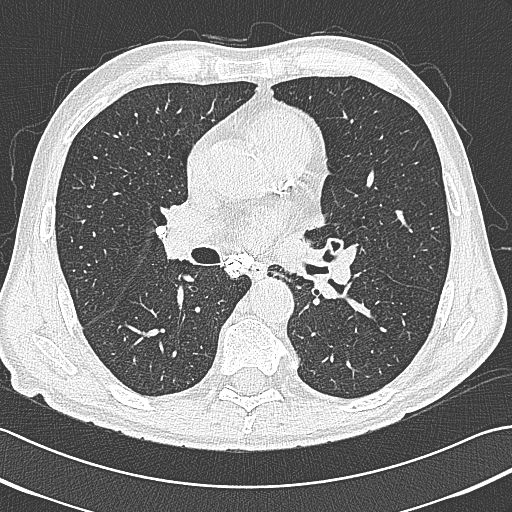
Axial slice from a low-dose chest CT screening exam; baseline screening round; lung window (W 1500 / L -600 HU); 1 mm slice thickness; lung (sharp) reconstruction kernel (B80f); 120 kVp; 512 × 512 image matrix. Male participant, aged 65 years at enrolment. Current smoker at enrolment.
- Expert-annotated lung lesion, bounding box [x1, y1, x2, y2] px = [305, 232, 354, 274].
- Screening reader's record for this exam: no non-calcified nodule ≥4 mm recorded.
- Participant outcome: lung cancer diagnosed 161 days after this screen — large cell neuroendocrine carcinoma, left hilum, left main stem bronchus, stage IIIB (AJCC 6th edition), 70 mm at pathology.